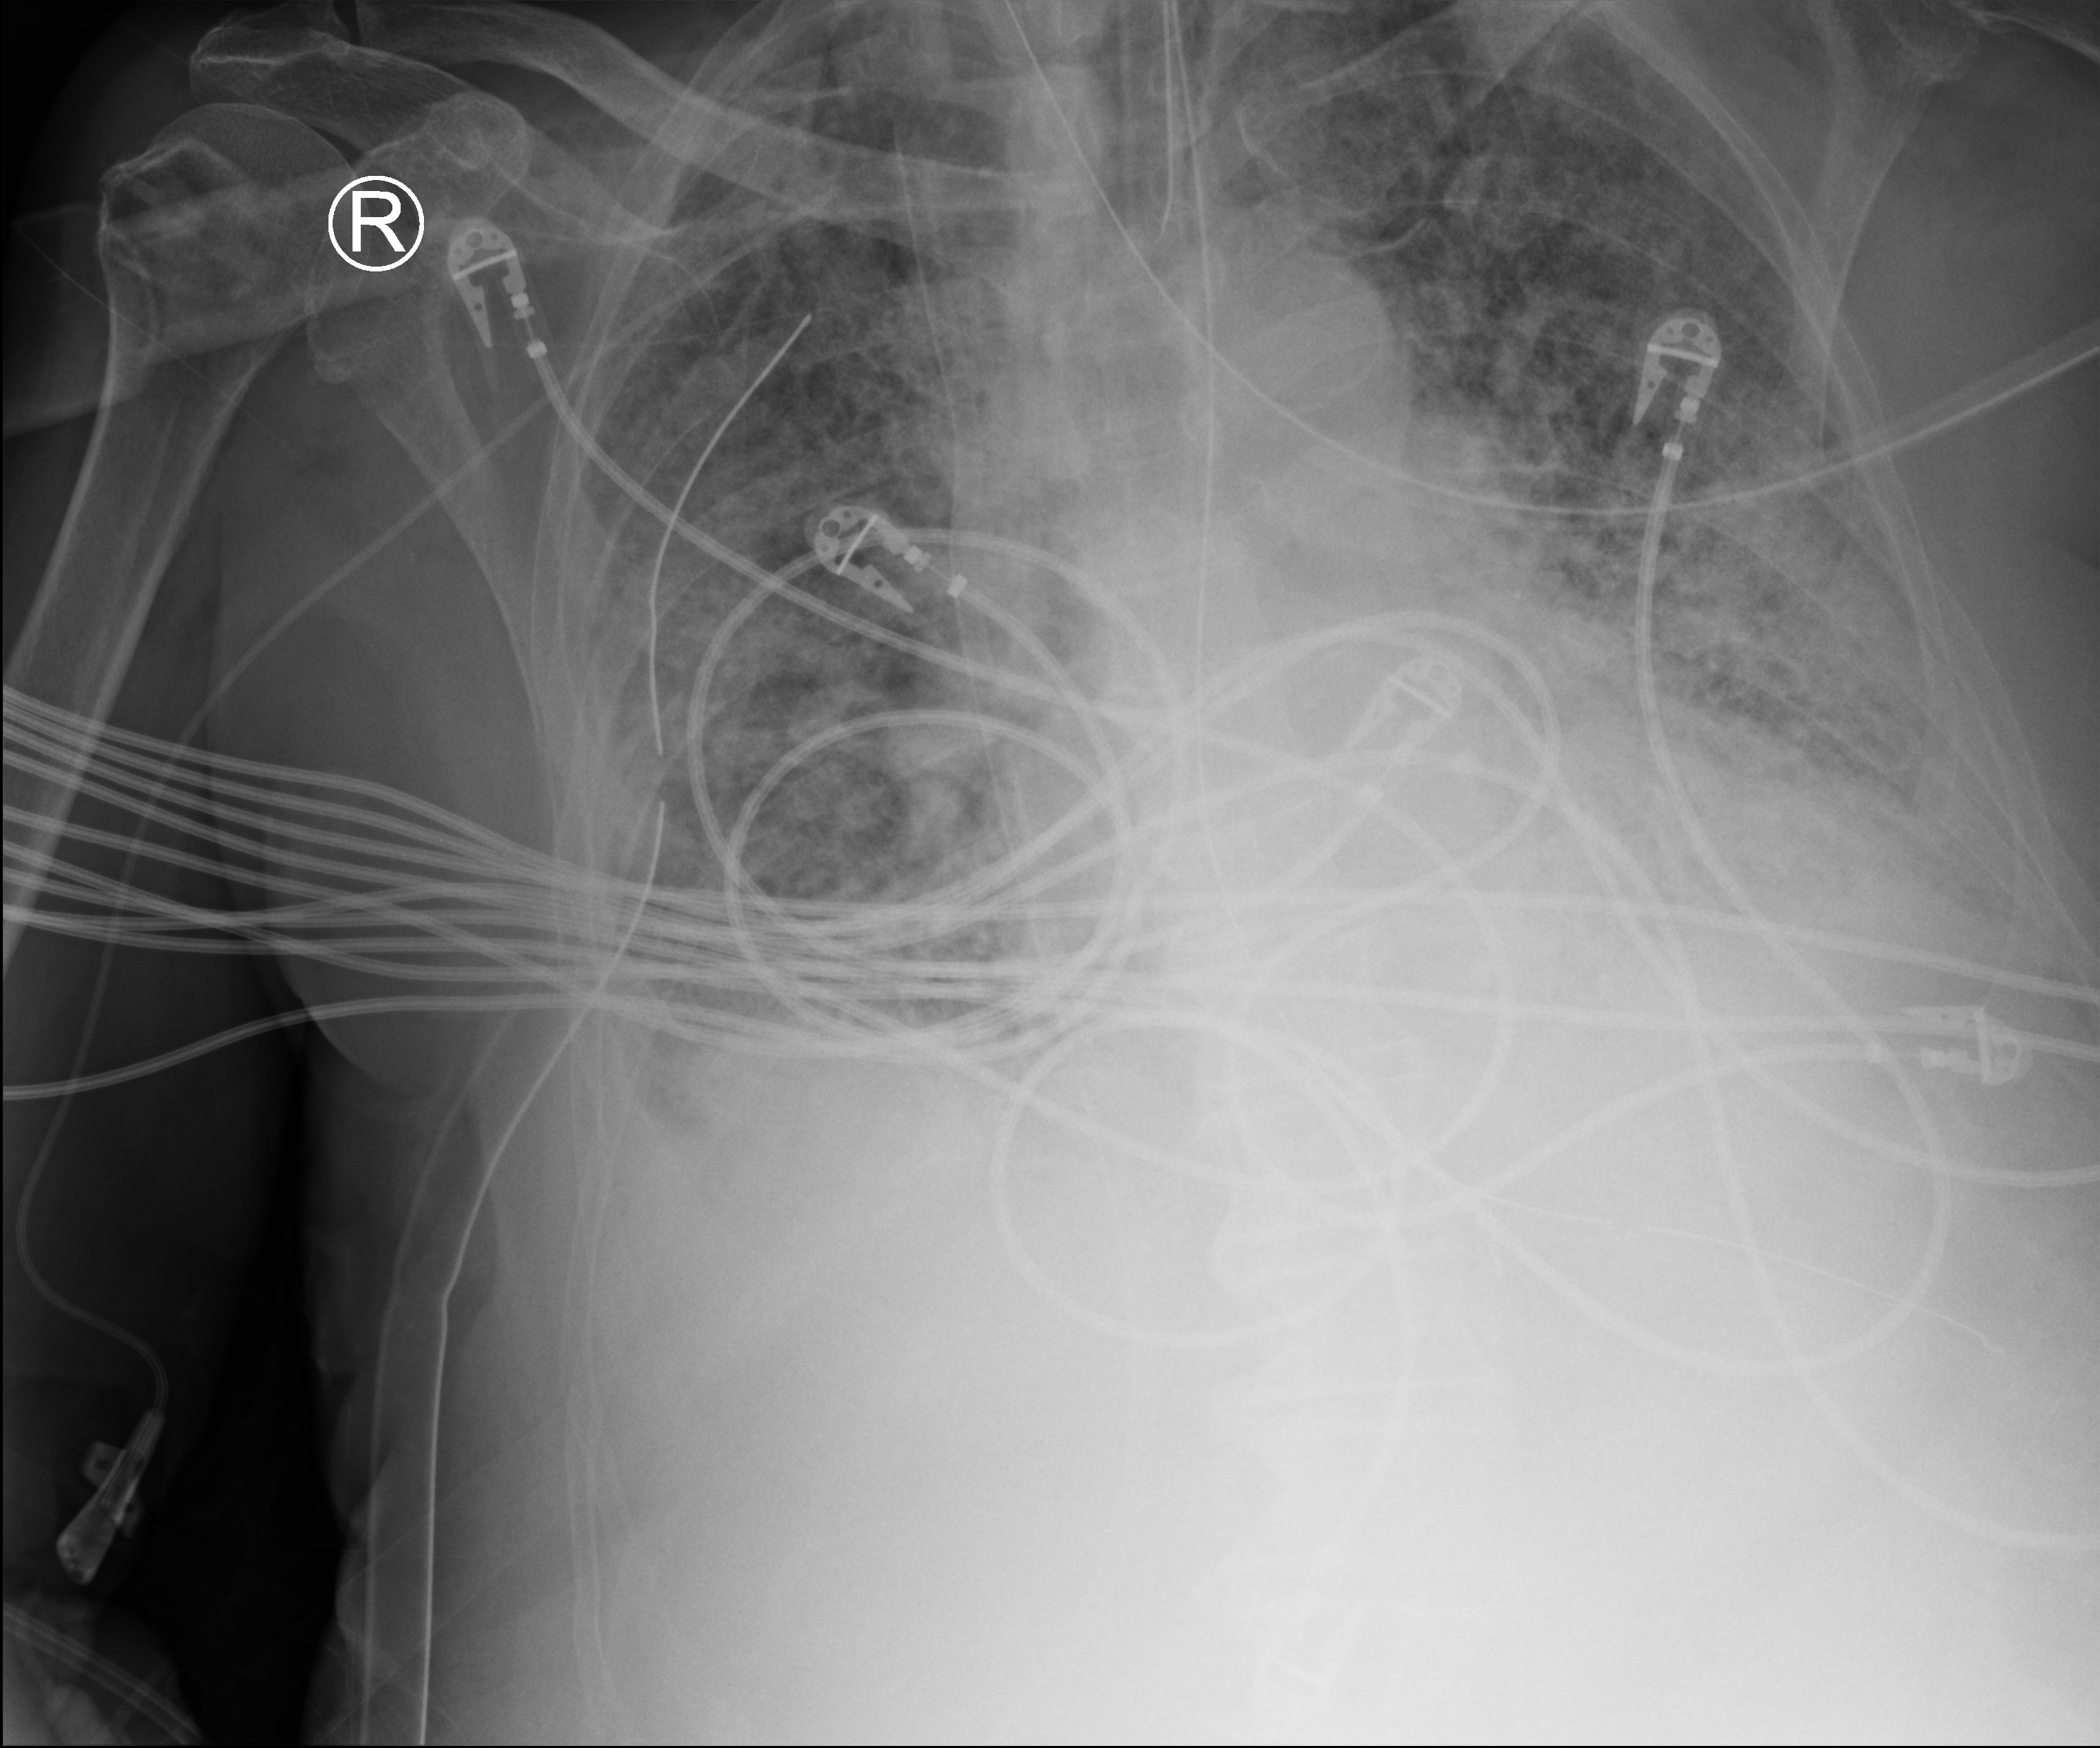
Portable chest radiograph; anteroposterior (AP) projection. Patient hospitalised with COVID-19; male, aged 75–90 years.
Admission-level facts for this patient (not findings on this image; timing relative to this image not recorded):
- length of hospital stay: 47 days
- diabetes (admission record): no